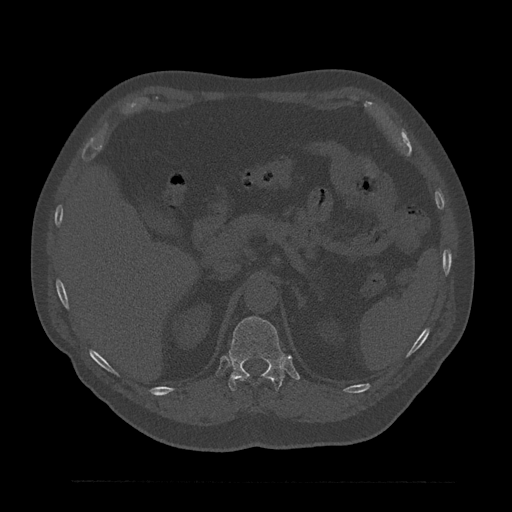
CT including the spine, one axial slice. Position 246 of 797 along the scan axis. Reconstruction kernel Br40s/3. 120 kVp. Bone window (W 1800 / L 400 HU). 0.5 mm slice thickness. 512 × 512 image matrix, field of view 430 × 430 mm. Patient: male, 61 years. Case-level facts recorded for this patient, not image findings: primary cancer: prostate.
Structures marked on this image (semi-automatic segmentation, software-assisted and operator-edited):
- T12 vertebra: bounding box (x1, y1, x2, y2) in pixels: (228, 317, 285, 392)